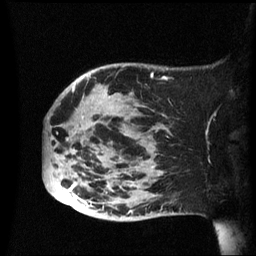
Breast MRI (dynamic contrast-enhanced), one sagittal slice; slice 17 of 60 in the series (ordered by position); dynamic contrast-enhanced series, image 2 of 3 at this slice position (ordered by acquisition); 1.5 T; TE 4.2 ms, TR 8.4 ms; 2.4 mm slice thickness; 256 × 256 image matrix. Patient: female, 49 years.
Structures marked on this image (semi-automatically segmented with operator editing):
- analysis volume of interest (the breast-tissue region the enhancement analysis was run in; not a lesion): bounding box [x1, y1, x2, y2] px = [43, 63, 174, 221]
- tumour enhancement mask (voxels above the 70 % enhancement threshold inside the analysis volume of interest): [66, 89, 154, 219]